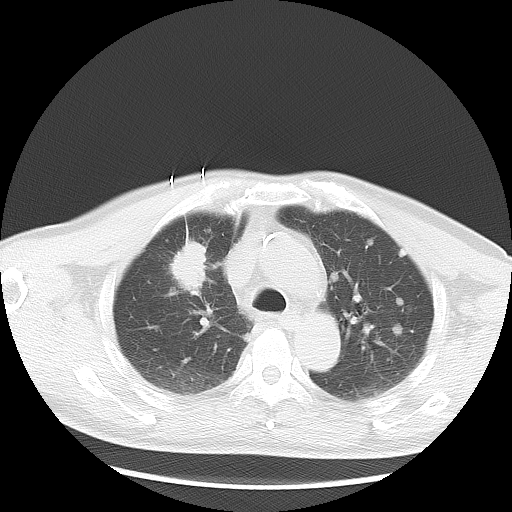
Chest CT, one axial slice; position 21 of 36 along the scan axis; 120 kVp; lung window (W 1500 / L -600 HU); 5 mm slice thickness; 512 × 512 image matrix, field of view 369 × 369 mm. Male patient, age 57 years. Case-level facts recorded for this patient, not image findings: clinical TNM (as recorded): T2 N3 M1a.
Annotated regions visible in this slice (rectangle marked by the reading radiologist):
- lung tumour (recorded histology: adenocarcinoma): bounding box [x1, y1, x2, y2] px = [165, 234, 210, 300]